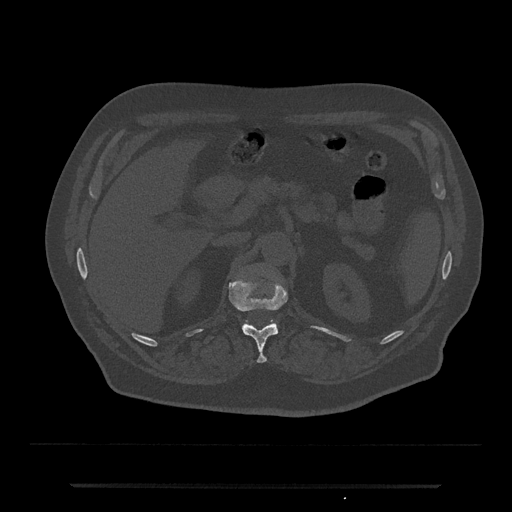
CT including the spine, one axial slice. Position 581 of 797 along the scan axis. Reconstruction kernel Br40s/3. 120 kVp. Bone window (W 1800 / L 400 HU). 0.5 mm slice thickness. 512 × 512 image matrix. Male patient, age 80 years. From the clinical record (not read from this slice): primary cancer: prostate; vertebrae with lytic lesions (as recorded): L1, T11.
Annotated regions visible in this slice (semi-automatically segmented with operator editing):
- L1 vertebra: bounding box (x1, y1, x2, y2) in pixels: (243, 321, 277, 325)
- T12 vertebra: (229, 280, 288, 363)